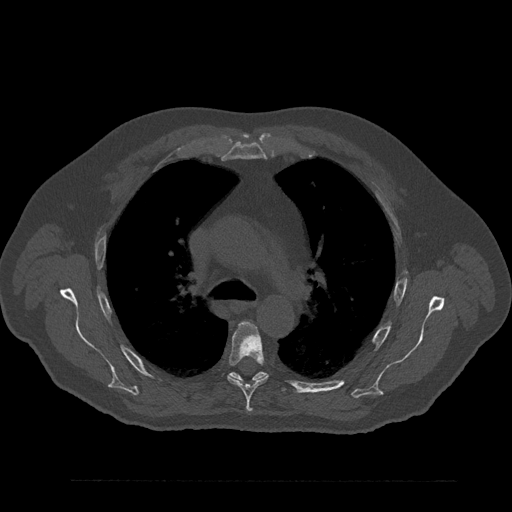
CT including the spine, one axial slice. Position 593 of 797 along the scan axis. 120 kVp. Bone window (W 1800 / L 400 HU). 0.5 mm slice thickness. 512 × 512 image matrix. Male patient, age 61 years. From the clinical record (not read from this slice): primary cancer: prostate.
Annotated regions visible in this slice (semi-automatically segmented with operator editing):
- T5 vertebra: bounding box (x1, y1, x2, y2) in pixels: (228, 322, 268, 412)
- T6 vertebra: (228, 364, 288, 392)